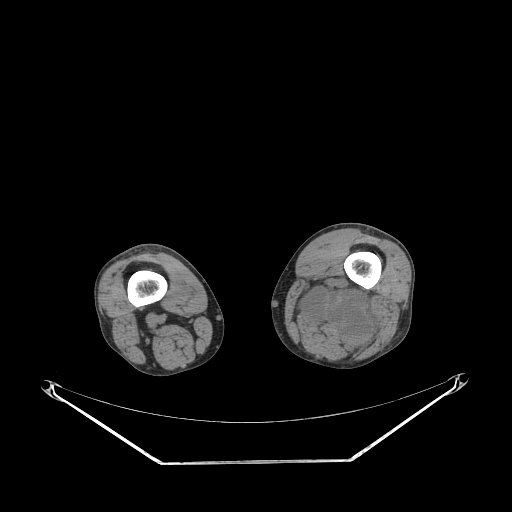
CT of an extremity soft-tissue mass (from a PET/CT study), one axial slice; slice 206 of 267 in the series (ordered by position); reconstruction kernel STANDARD; 140 kVp; soft-tissue window (W 400 / L 40 HU); 3.75 mm slice thickness; 512 × 512 image matrix, field of view 500 × 500 mm. Male patient. From the clinical record (not read from this slice): histological type: undifferentiated pleomorphic liposarcoma; grade: high; site of the primary tumour: left thigh.
Structures marked on this image (expert contour drawn on MRI and transferred to this co-registered scan by the dataset authors):
- gross tumour volume including surrounding oedema: bounding box (x1, y1, x2, y2) in pixels: (292, 276, 375, 357)
- gross tumour volume (mass): (329, 297, 364, 332)